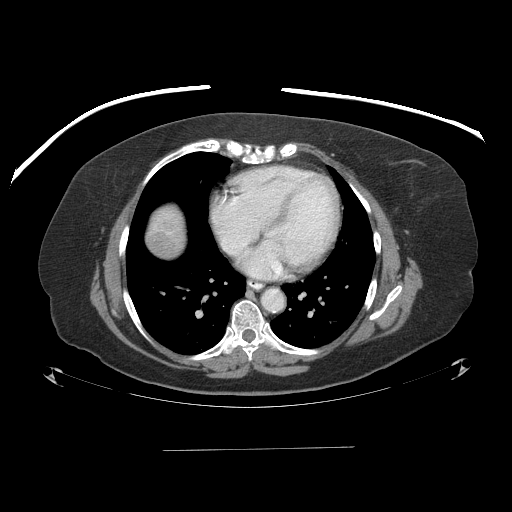
Contrast-enhanced abdominal CT (liver protocol), one axial slice; position 89 of 103 along the scan axis; 120 kVp; one of 2 acquisitions stored at this slice position; soft-tissue window (W 400 / L 40 HU); 2.5 mm slice thickness; 512 × 512 image matrix, field of view 500 × 500 mm. From the clinical record (not read from this slice): diagnosis: hepatocellular carcinoma (patient treated with transarterial chemoembolisation; whether this scan precedes or follows treatment is not stated here); TNM stage (as recorded): Stage-IIIA; Child-Pugh class: A; tumour differentiation: poorly differentiated; tumour nodularity: multinodular.
Outlined on this slice (semi-automatic segmentation, software-assisted and operator-edited):
- liver parenchyma outside the tumour (the mass and vessels are separate outlines, so this box may not span the whole liver): bounding box <146,206,184,256> (left, top, right, bottom; pixels)